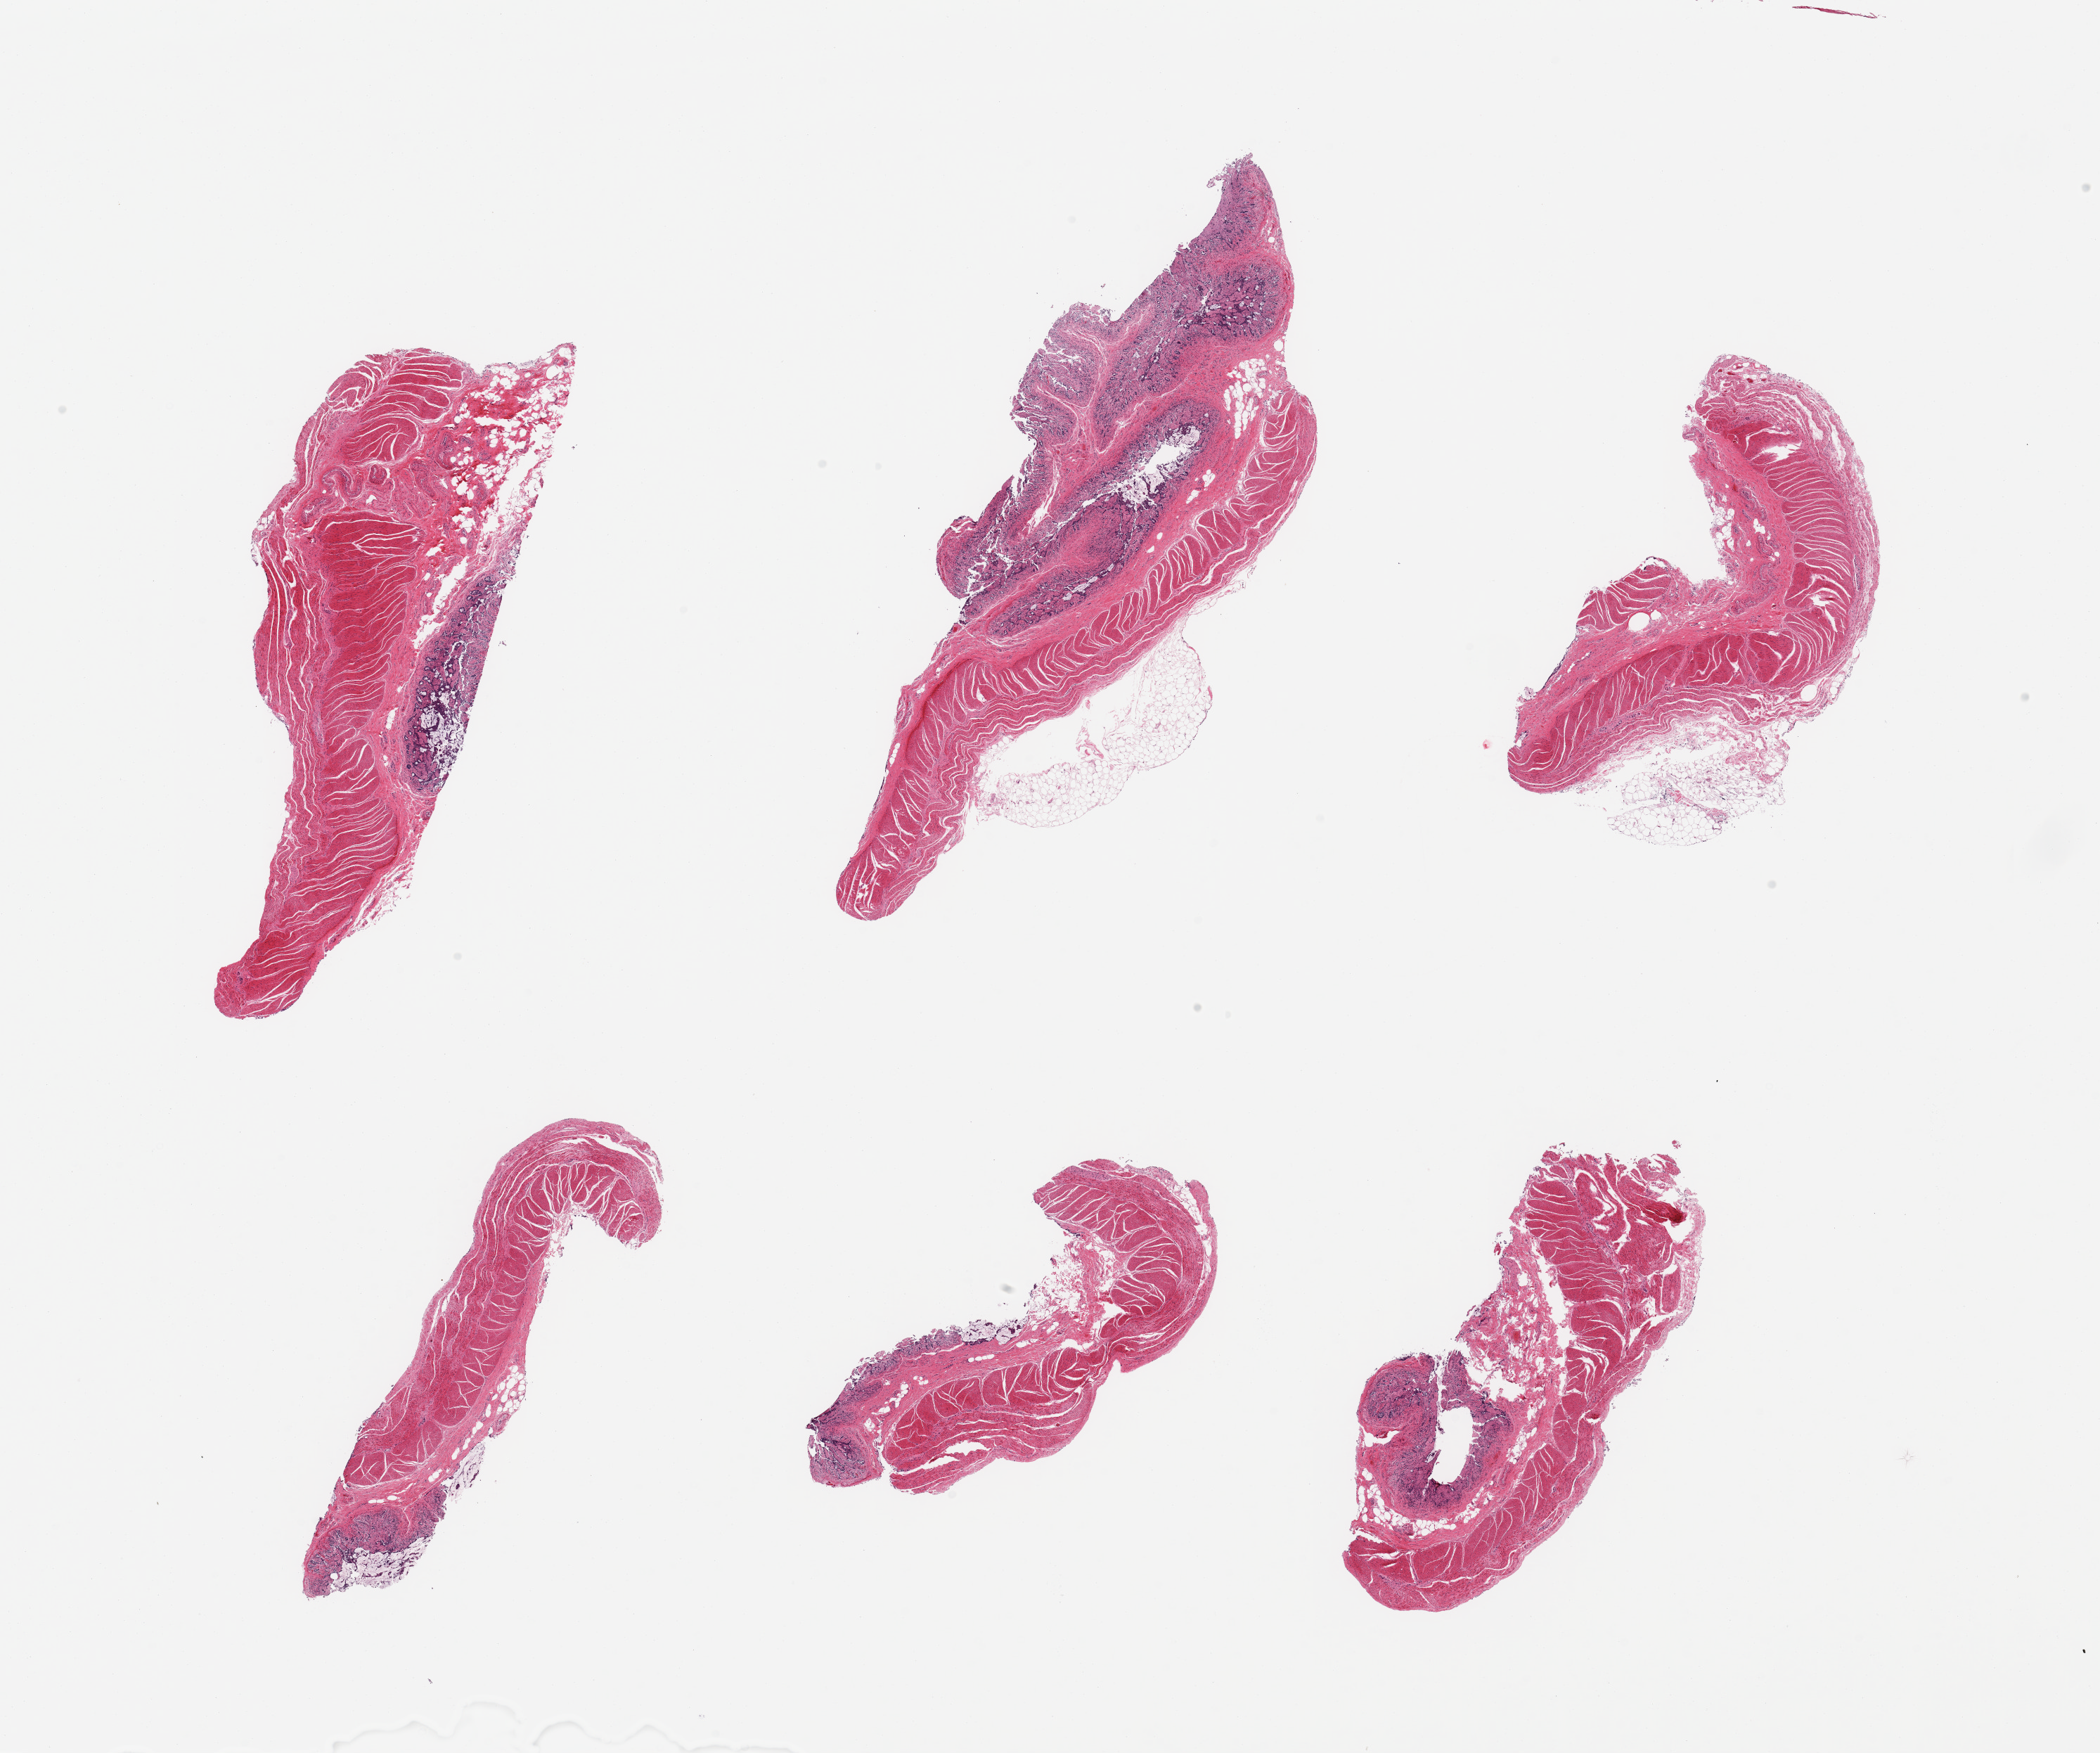
Hematoxylin and eosin (H&E) whole-slide image — whole scanned area (about 23.6 x 19.7 mm, from a 20x scan) shown as a low-resolution overview, PAXgene-fixed, paraffin-embedded tissue, sampled site (target tissue): ileum, donor tissue sample. Male donor.
• review note (as recorded): 6 pieces, mucosa with advance autolysis, devoid of lymphoid aggregates